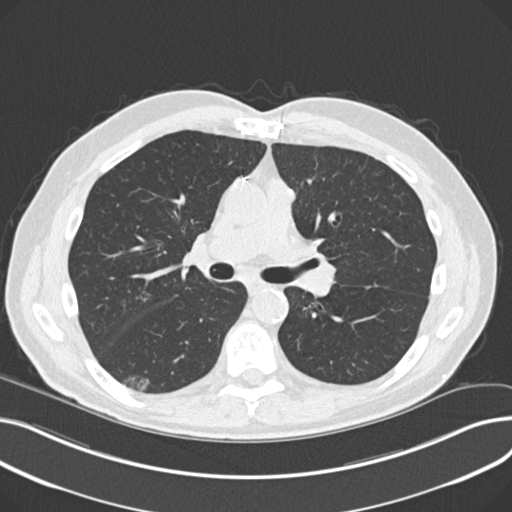
Chest CT (low-dose screening protocol), one axial image; third annual screen; lung window (W 1500 / L -600 HU); standard (soft-tissue) reconstruction kernel (B30f); slice 103 of 230 in the series; 512 × 512 image matrix, field of view 372 × 372 mm. Male participant, aged 68 years at enrolment.
Lesion marked by an expert reader, bounding box <121,367,164,398> (left, top, right, bottom; pixels). The screening reader recorded 5 non-calcified nodules or masses ≥4 mm on this exam (right upper lobe, left upper lobe, right upper lobe, right lower lobe, right upper lobe); which of them this box marks is not recorded. Official screen result: positive, other. Later outcome: lung cancer diagnosed 247 days after this screen — non-small cell carcinoma, right lower lobe, poorly differentiated (G3), stage IA (AJCC 6th edition), 23 mm at pathology.